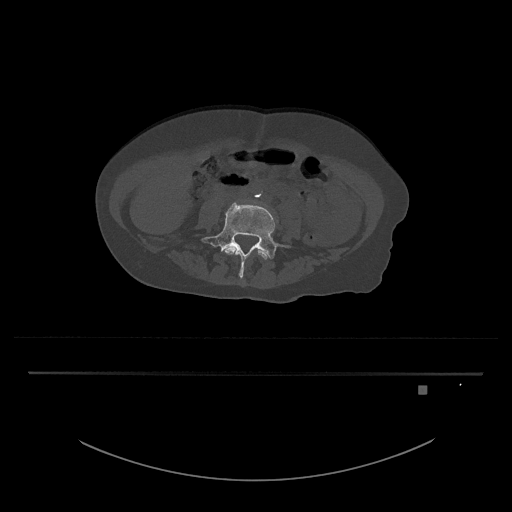
CT including the spine, one axial slice; slice 320 of 797 in the series (ordered by position); bone window (W 1800 / L 400 HU); 0.5 mm slice thickness; 512 × 512 image matrix, field of view 500 × 500 mm. Female patient, age 57 years. From the clinical record (not read from this slice): primary cancer: cervical.
Annotated regions visible in this slice (semi-automatically segmented with operator editing):
- L4 vertebra: bounding box [x1, y1, x2, y2] px = [224, 246, 270, 260]